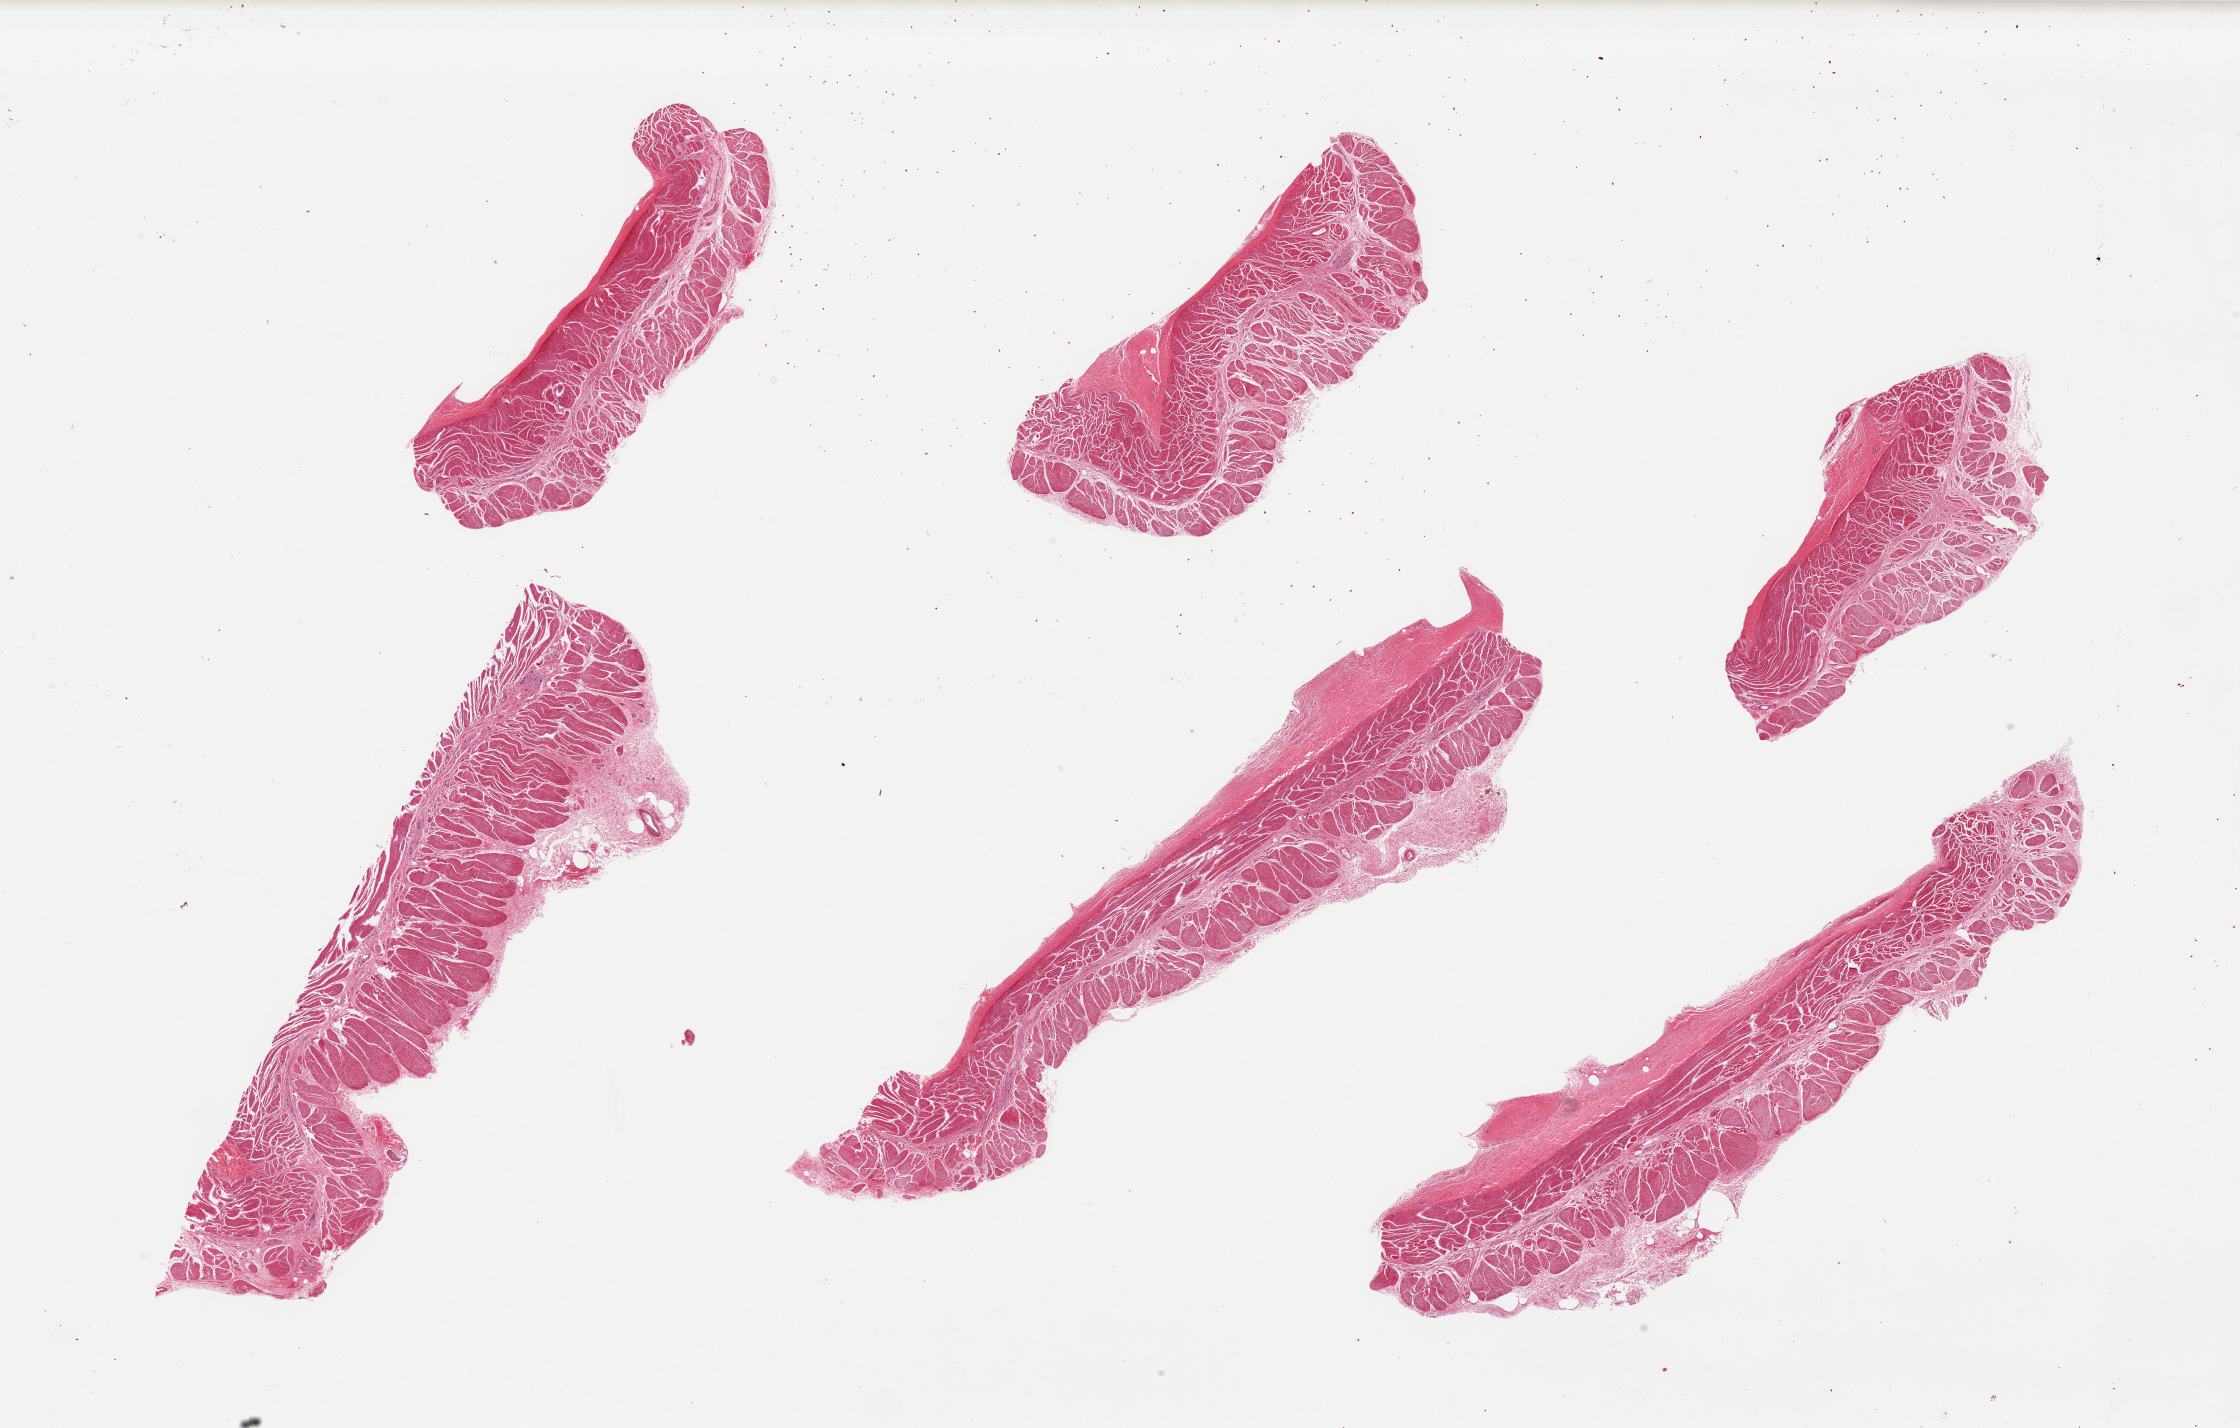
Digitized H&E-stained section — shown as a low-resolution overview of the whole scanned area (about 35.4 x 22.6 mm); PAXgene-fixed paraffin-embedded (PFPE) section; section of esophageal muscle (target tissue); tissue donor sample. Female donor.
* pathologist's review note for this sample: 6 pieces, 10% external fat